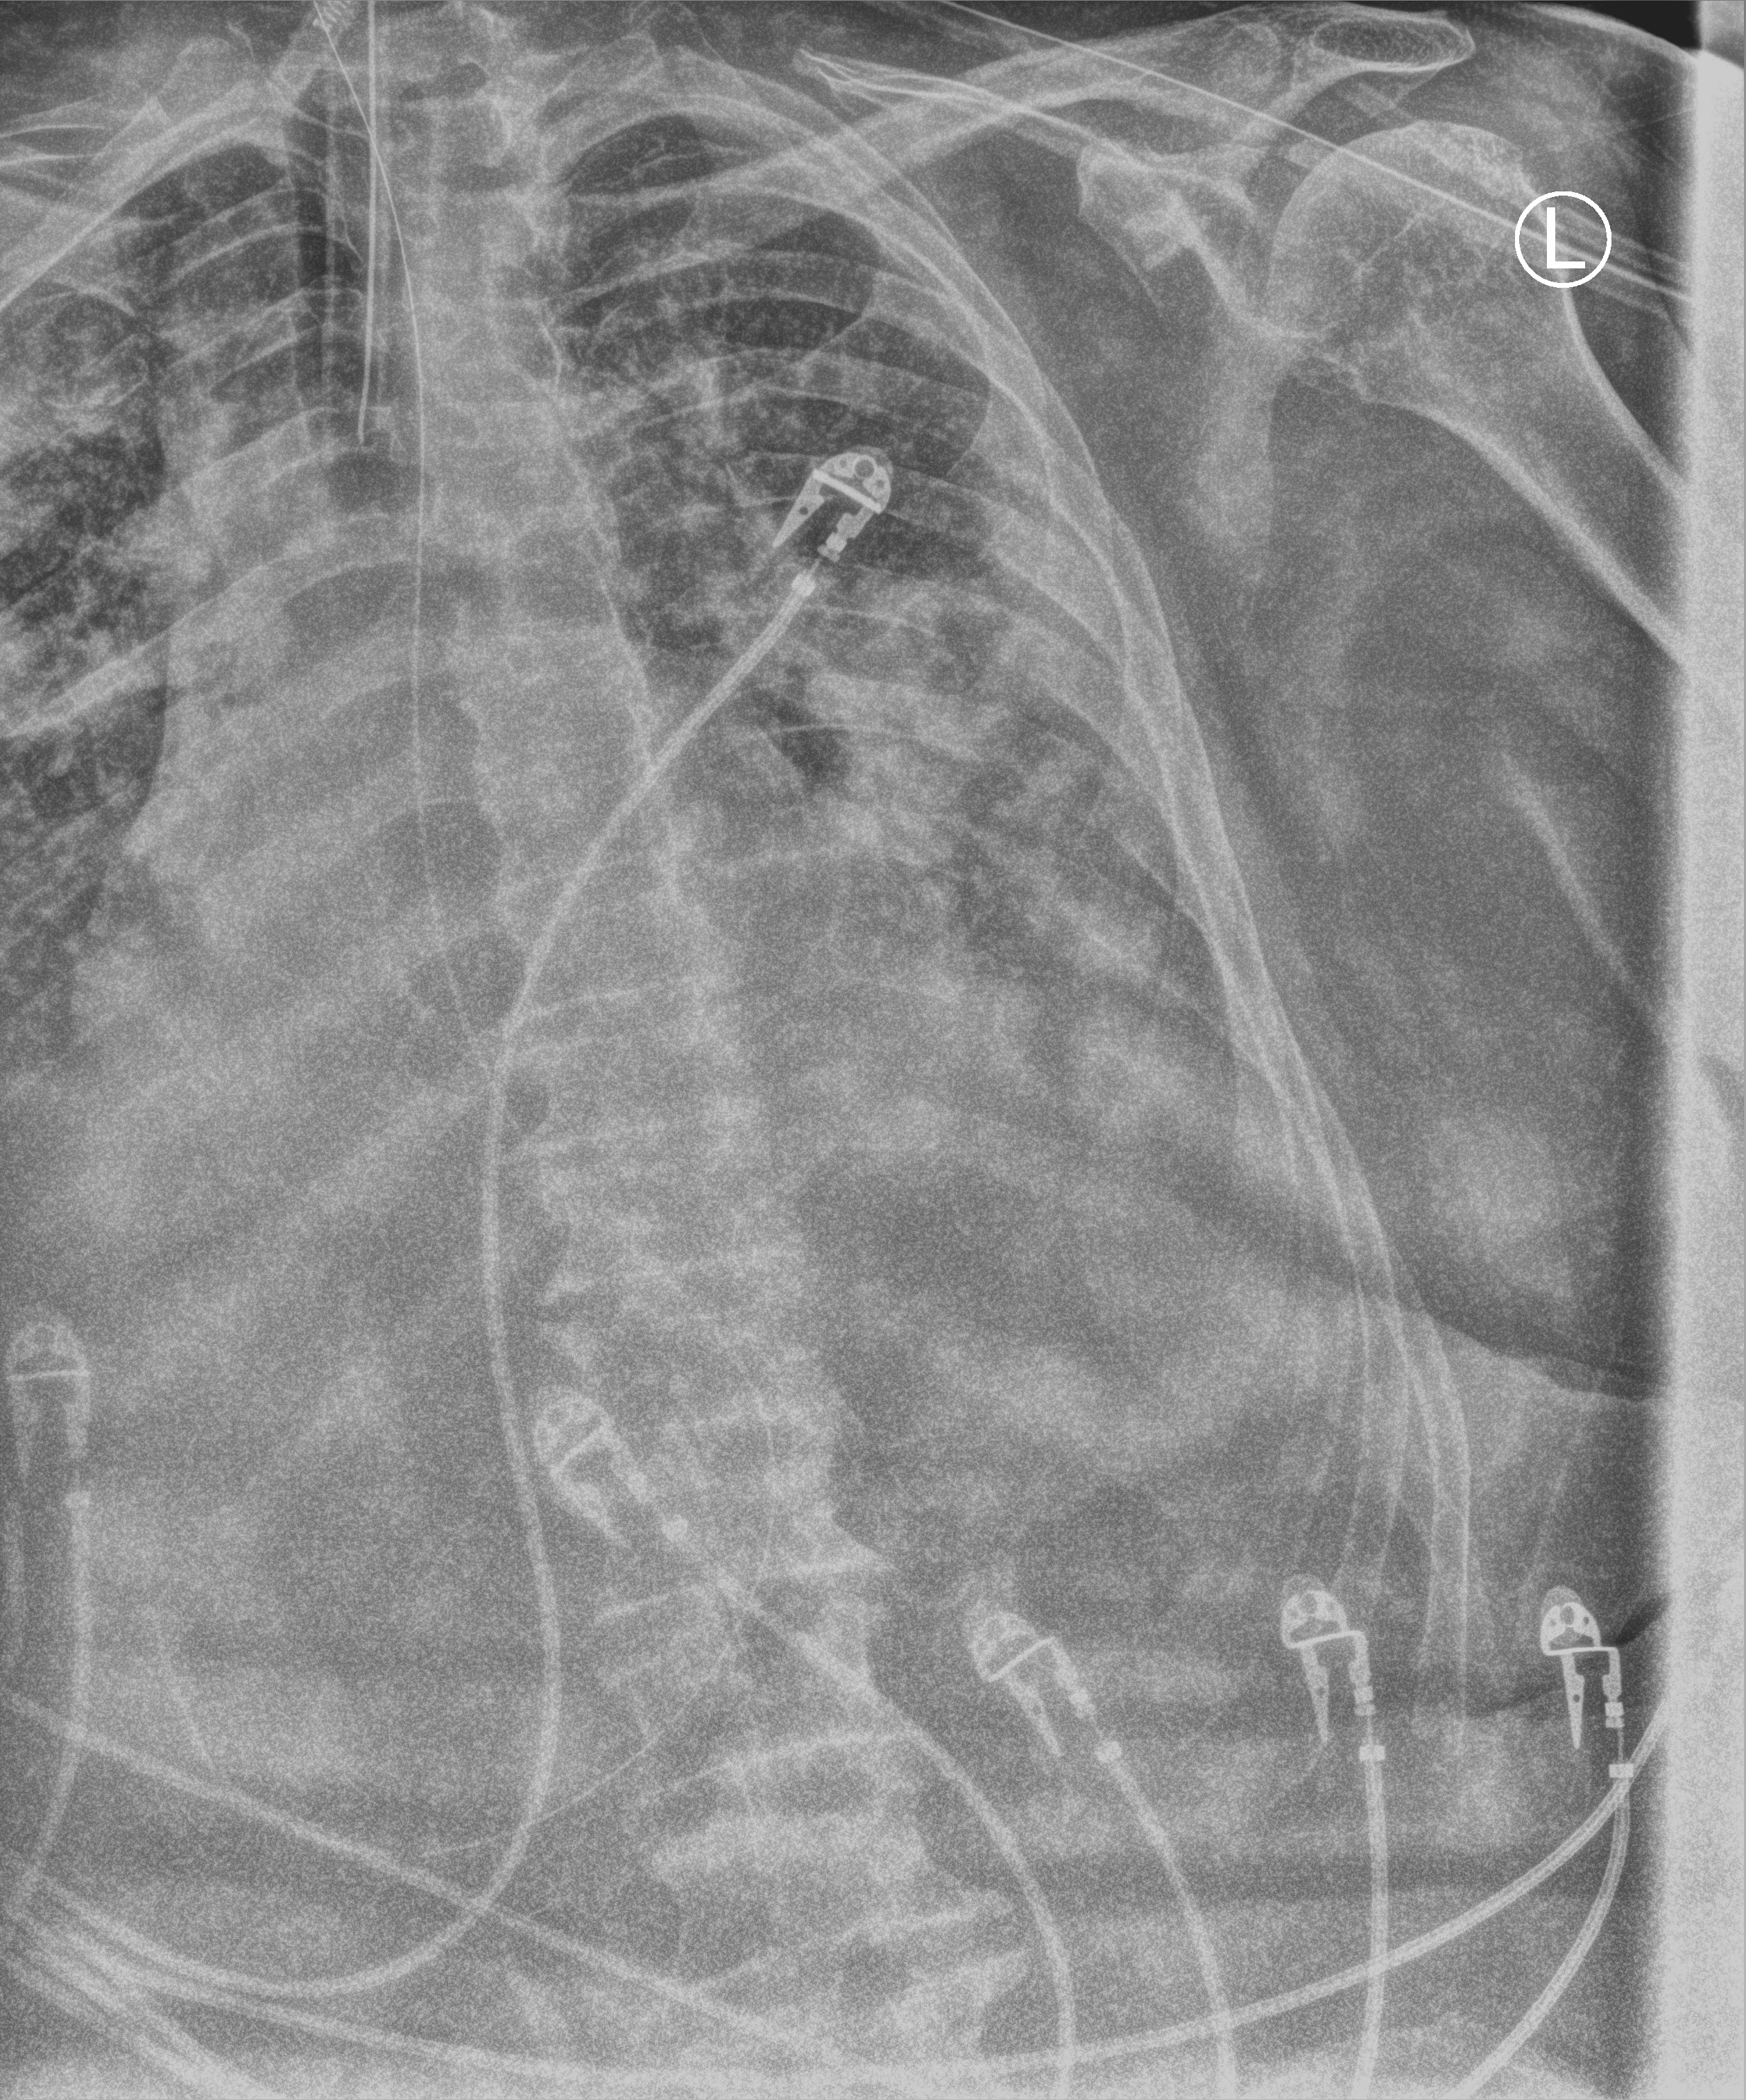
Bedside chest radiograph (computed radiography), anteroposterior (AP) projection. Male patient hospitalised with COVID-19, age 60–74 years.
Hospital-stay facts (about this admission, not read from this image; timing relative to this image not recorded):
- admitted to intensive care during this hospital stay: yes
- mechanically ventilated during this hospital stay: yes
- diabetes (admission record): yes